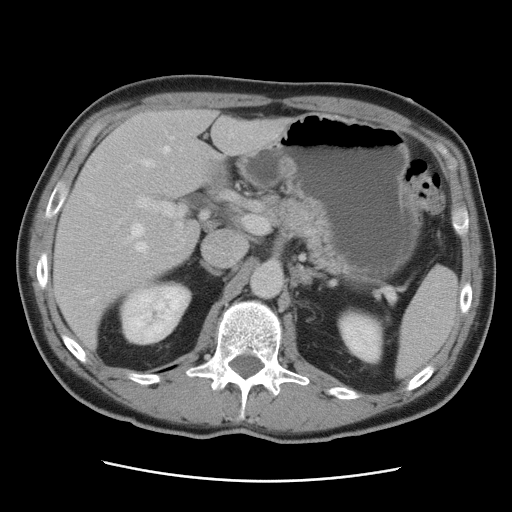
Contrast-enhanced abdominal CT, one axial slice; slice 53 of 89 in the series (ordered by position); 120 kVp; soft-tissue window (W 400 / L 40 HU); 512 × 512 image matrix, field of view 366 × 366 mm. Male patient, age 59 years. Case-level facts recorded for this patient, not image findings: diagnosis: colorectal cancer liver metastases, imaged before liver resection; multiple liver metastases: yes.
Annotated regions visible in this slice (manually delineated by an expert):
- hepatic veins: box from (x=78, y=134) to (x=238, y=305) px
- liver: (x=53, y=110)–(x=293, y=351)
- planned liver remnant (the part of the liver to remain after resection): (x=72, y=110)–(x=223, y=240)
- portal vein (with intrahepatic branches): (x=137, y=197)–(x=263, y=251)